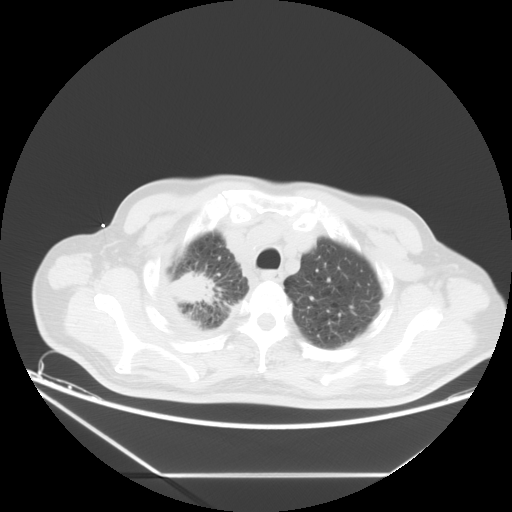
Chest CT, one axial slice. Position 16 of 20 along the scan axis. Reconstruction kernel STANDARD. 120 kVp. Lung window (W 1500 / L -600 HU). 5 mm slice thickness. 512 × 512 image matrix, field of view 418 × 418 mm. Patient: male, 75 years. From the clinical record (not read from this slice): clinical TNM (as recorded): T1c N1 M1.
Outlined on this slice (bounding box drawn by a radiologist):
- lung tumour (recorded histology: adenocarcinoma): bounding box <165,270,219,316> (left, top, right, bottom; pixels)